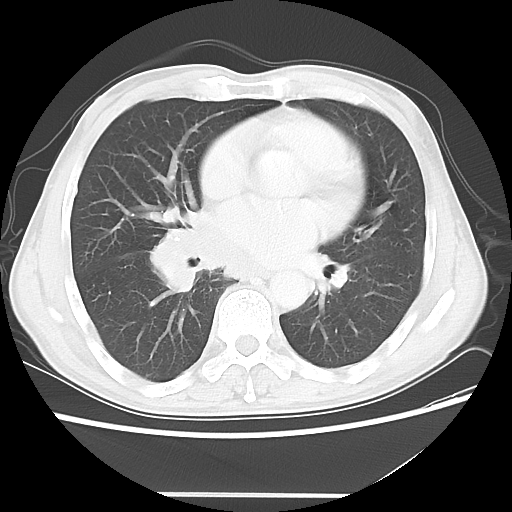
Chest CT, one axial slice; slice 25 of 56 in the series (ordered by position); reconstruction kernel LUNG; 120 kVp; lung window (W 1500 / L -600 HU); 512 × 512 image matrix, field of view 344 × 344 mm. Patient: male, 65 years. Case-level facts recorded for this patient, not image findings: clinical TNM (as recorded): T1c N3 M0; histopathological grade: G3.
Outlined on this slice (bounding box drawn by a radiologist):
- lung tumour (recorded histology: small cell carcinoma): bounding box [x1, y1, x2, y2] px = [152, 204, 255, 292]